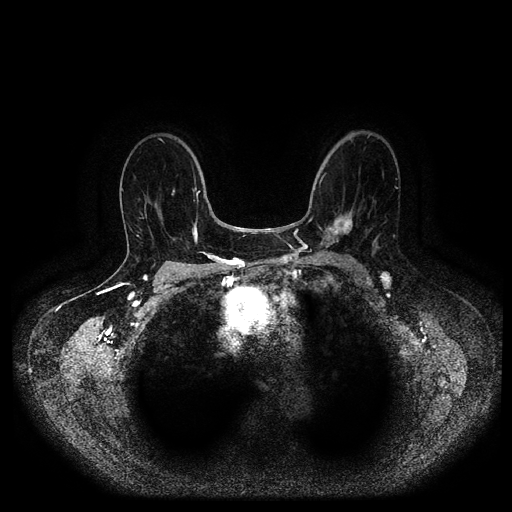
Breast MRI (dynamic contrast-enhanced, multi-phase), one axial slice. Position 58 of 116 along the scan axis. Dynamic contrast-enhanced series, time point 2 of 5 at this slice position (early post-contrast). 1.5 T. TE 2.6 ms, TR 5.2 ms. 2 mm slice thickness. 512 × 512 image matrix. Patient: female, 69 years.
Annotated regions visible in this slice (semi-automatic segmentation, software-assisted and operator-edited):
- breast lesion (labelled 'tumour' in the annotation; benign lesions carry a separate 'benign' label): box from (x=323, y=209) to (x=357, y=242) px